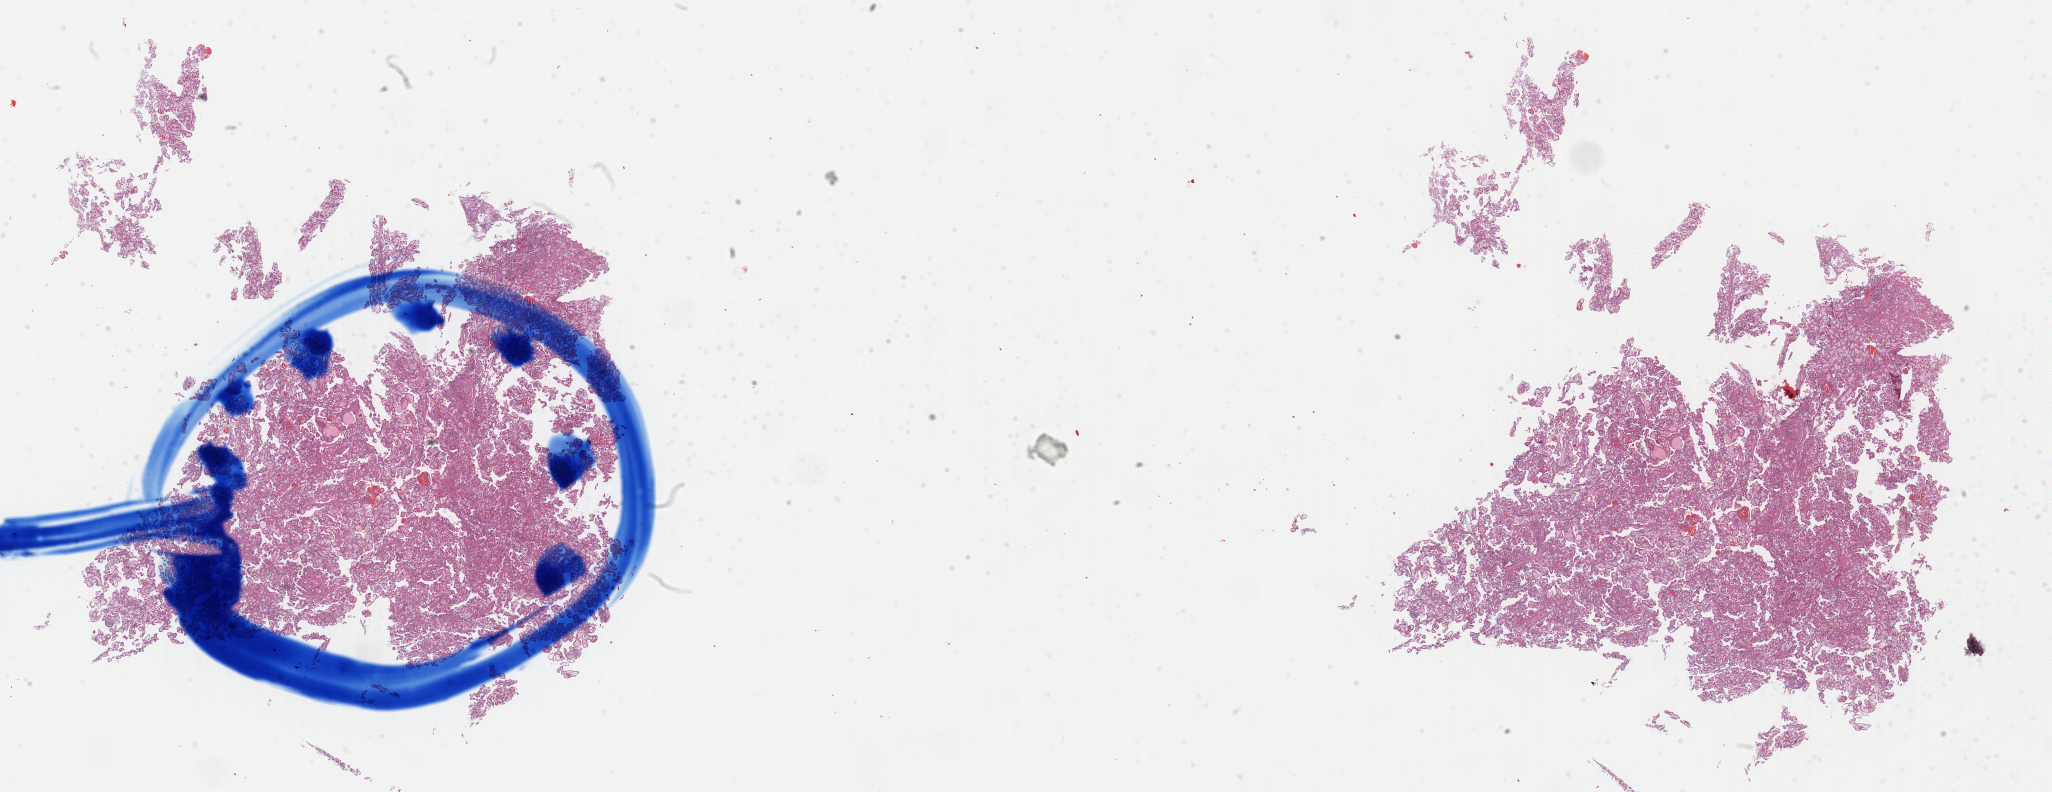
Hematoxylin and eosin (H&E) stained whole-slide image, shown as a low-resolution overview of the whole scanned area (about 32.4 x 12.5 mm, acquisition: 40x scan); FFPE section; kidney, primary tumour sample. Male, age 80 years at initial diagnosis.
Laterality: right. Histologic diagnosis: Papillary adenocarcinoma, NOS. AJCC pathologic stage: I.